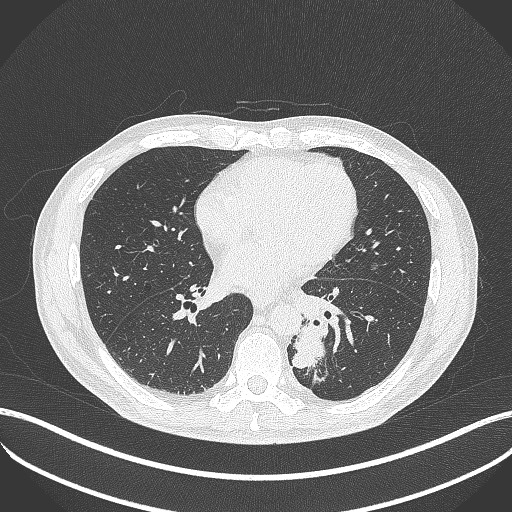
Chest CT, one axial slice; lung window (W 1500 / L -600 HU); 1 mm slice thickness; 512 × 512 image matrix, field of view 400 × 400 mm. Patient: male, 72 years. From the clinical record (not read from this slice): clinical TNM (as recorded): T2b N0 M1.
Structures marked on this image (bounding box drawn by a radiologist):
- lung tumour (recorded histology: adenocarcinoma): bounding box [x1, y1, x2, y2] px = [294, 318, 327, 376]